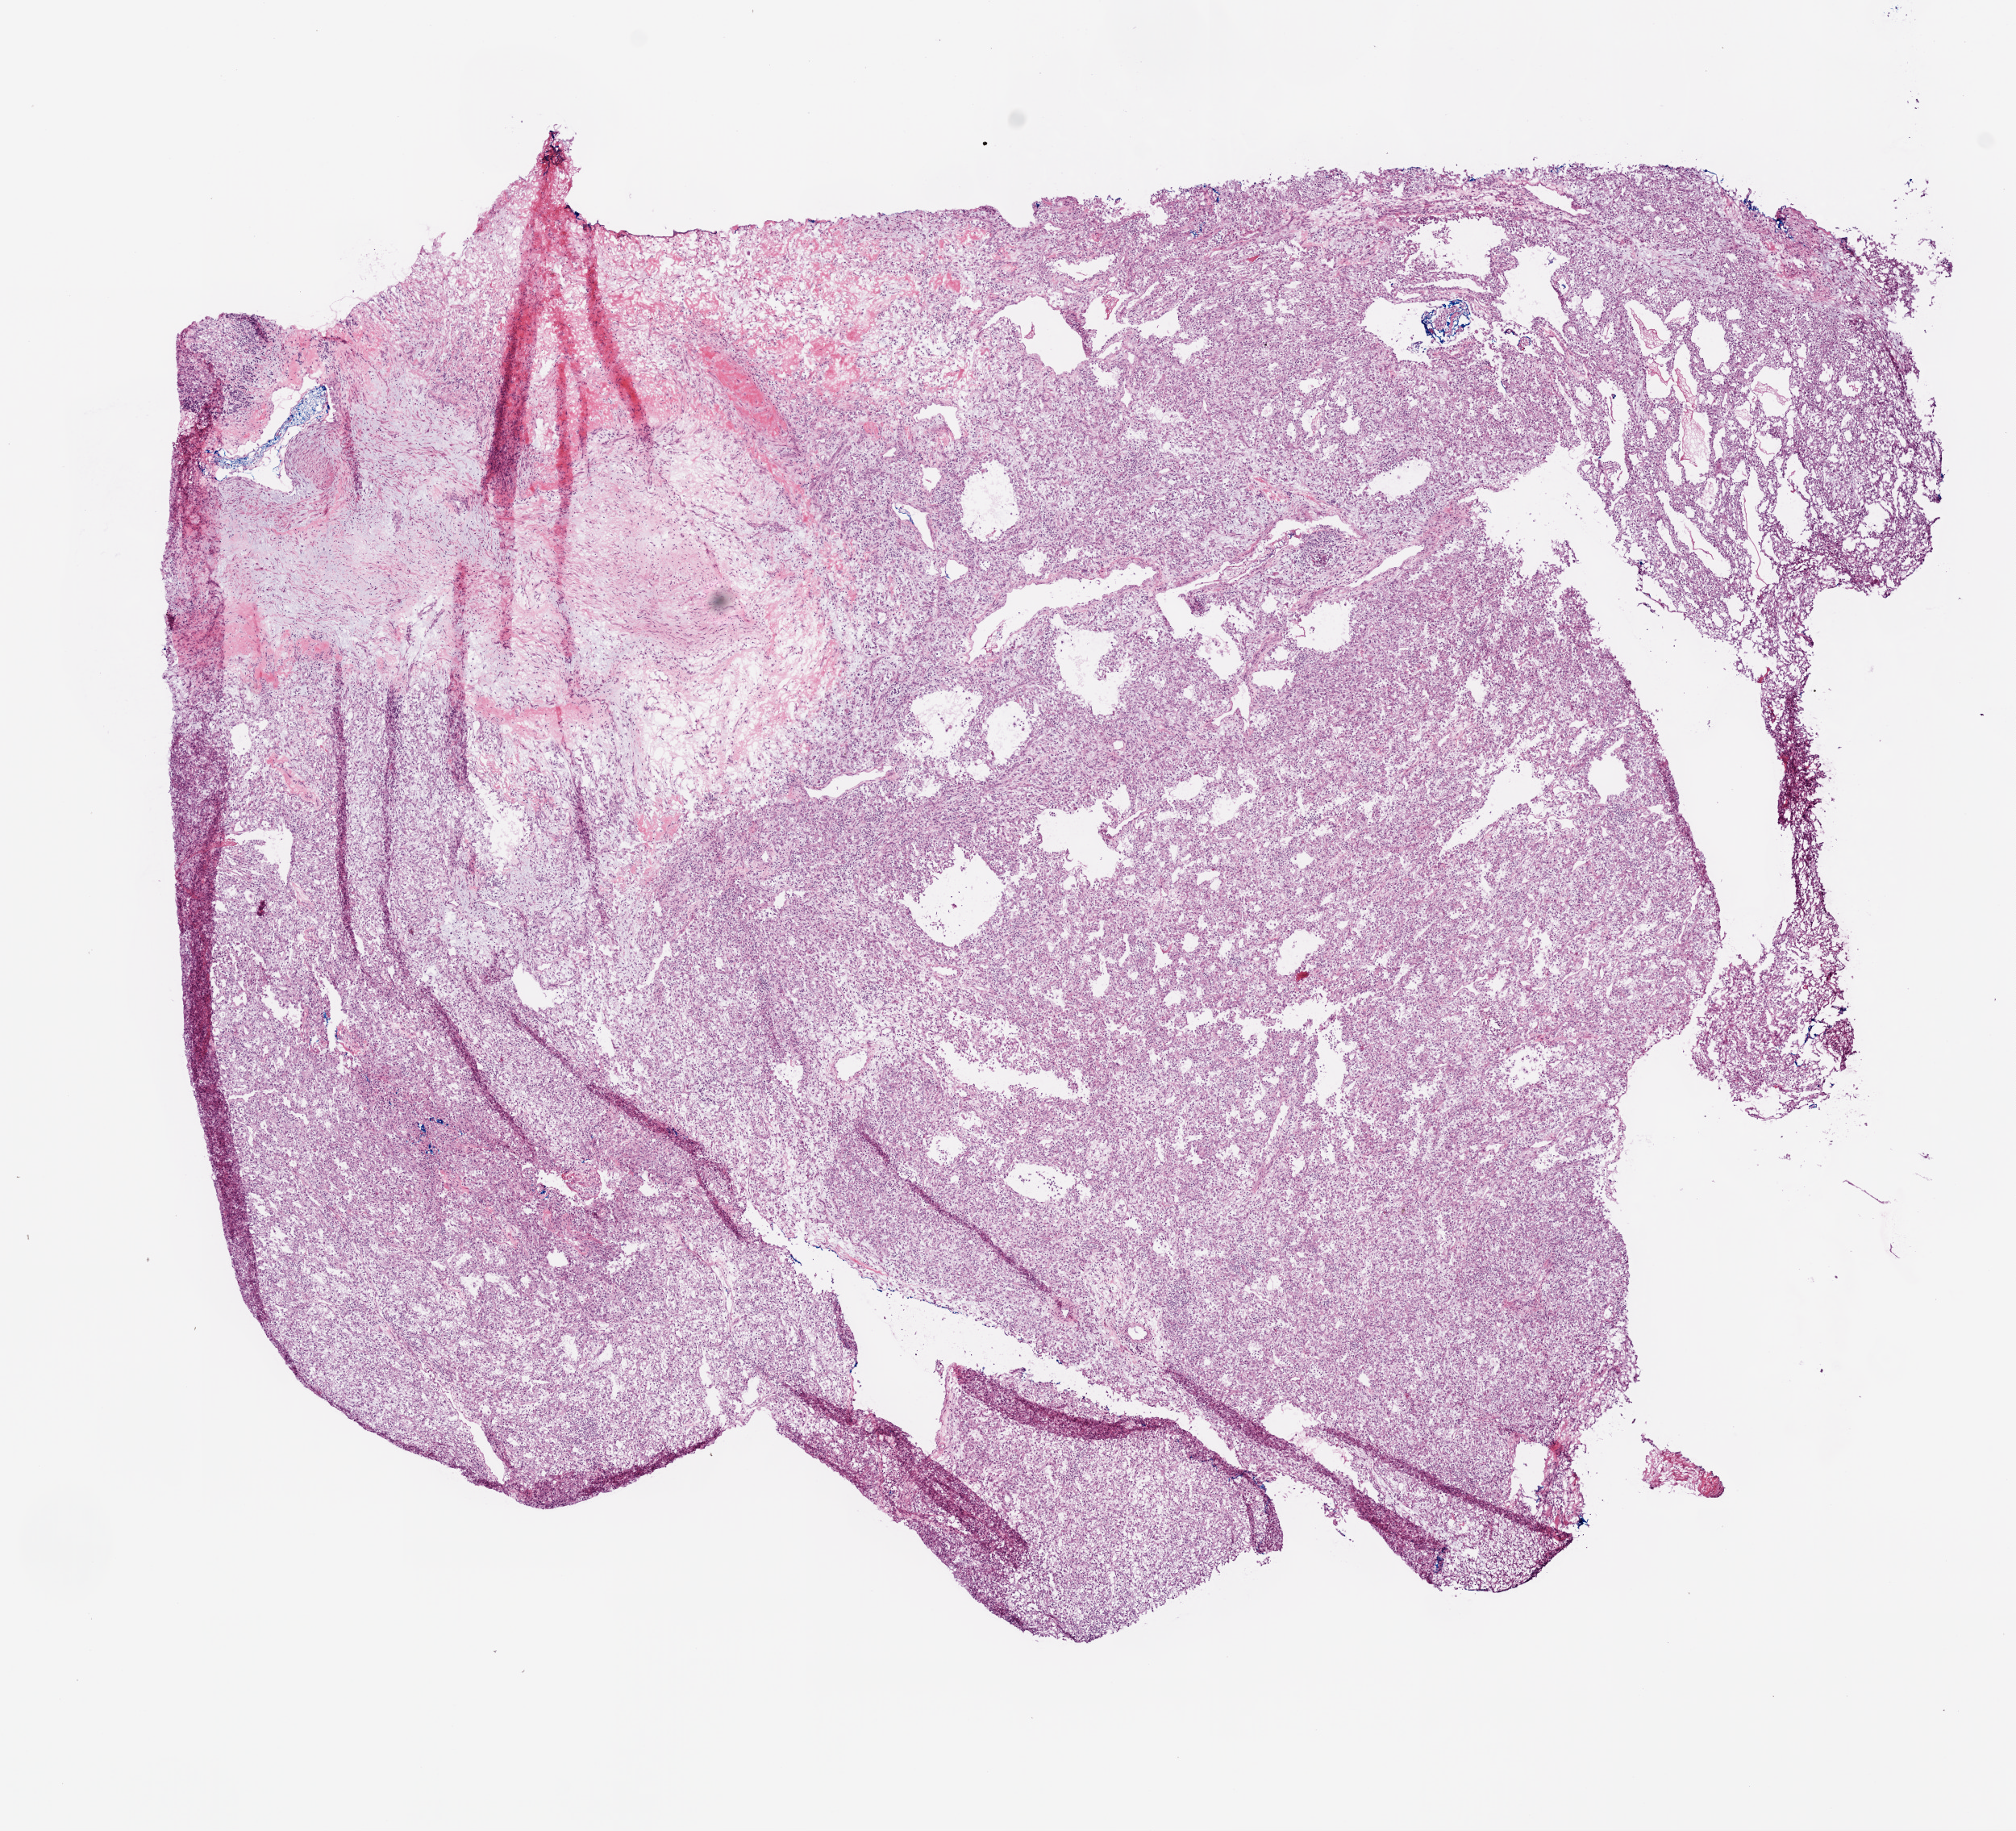
Whole-slide histology image, H&E — a low-resolution overview of the entire scanned area, about 10.0 x 9.1 mm (from a 20x scan), frozen section from the bottom of the tissue portion, sample: primary tumour, kidney. Female patient; age at initial diagnosis 63 years. Histologic grade: G3 (poorly differentiated). Composition of this section per pathologist review: tumour cells 80%, tumour nuclei 80%, normal cells 0%, stromal cells 20%, necrosis 0%.
- AJCC pathologic stage: III
- diagnosis: Clear cell adenocarcinoma, NOS